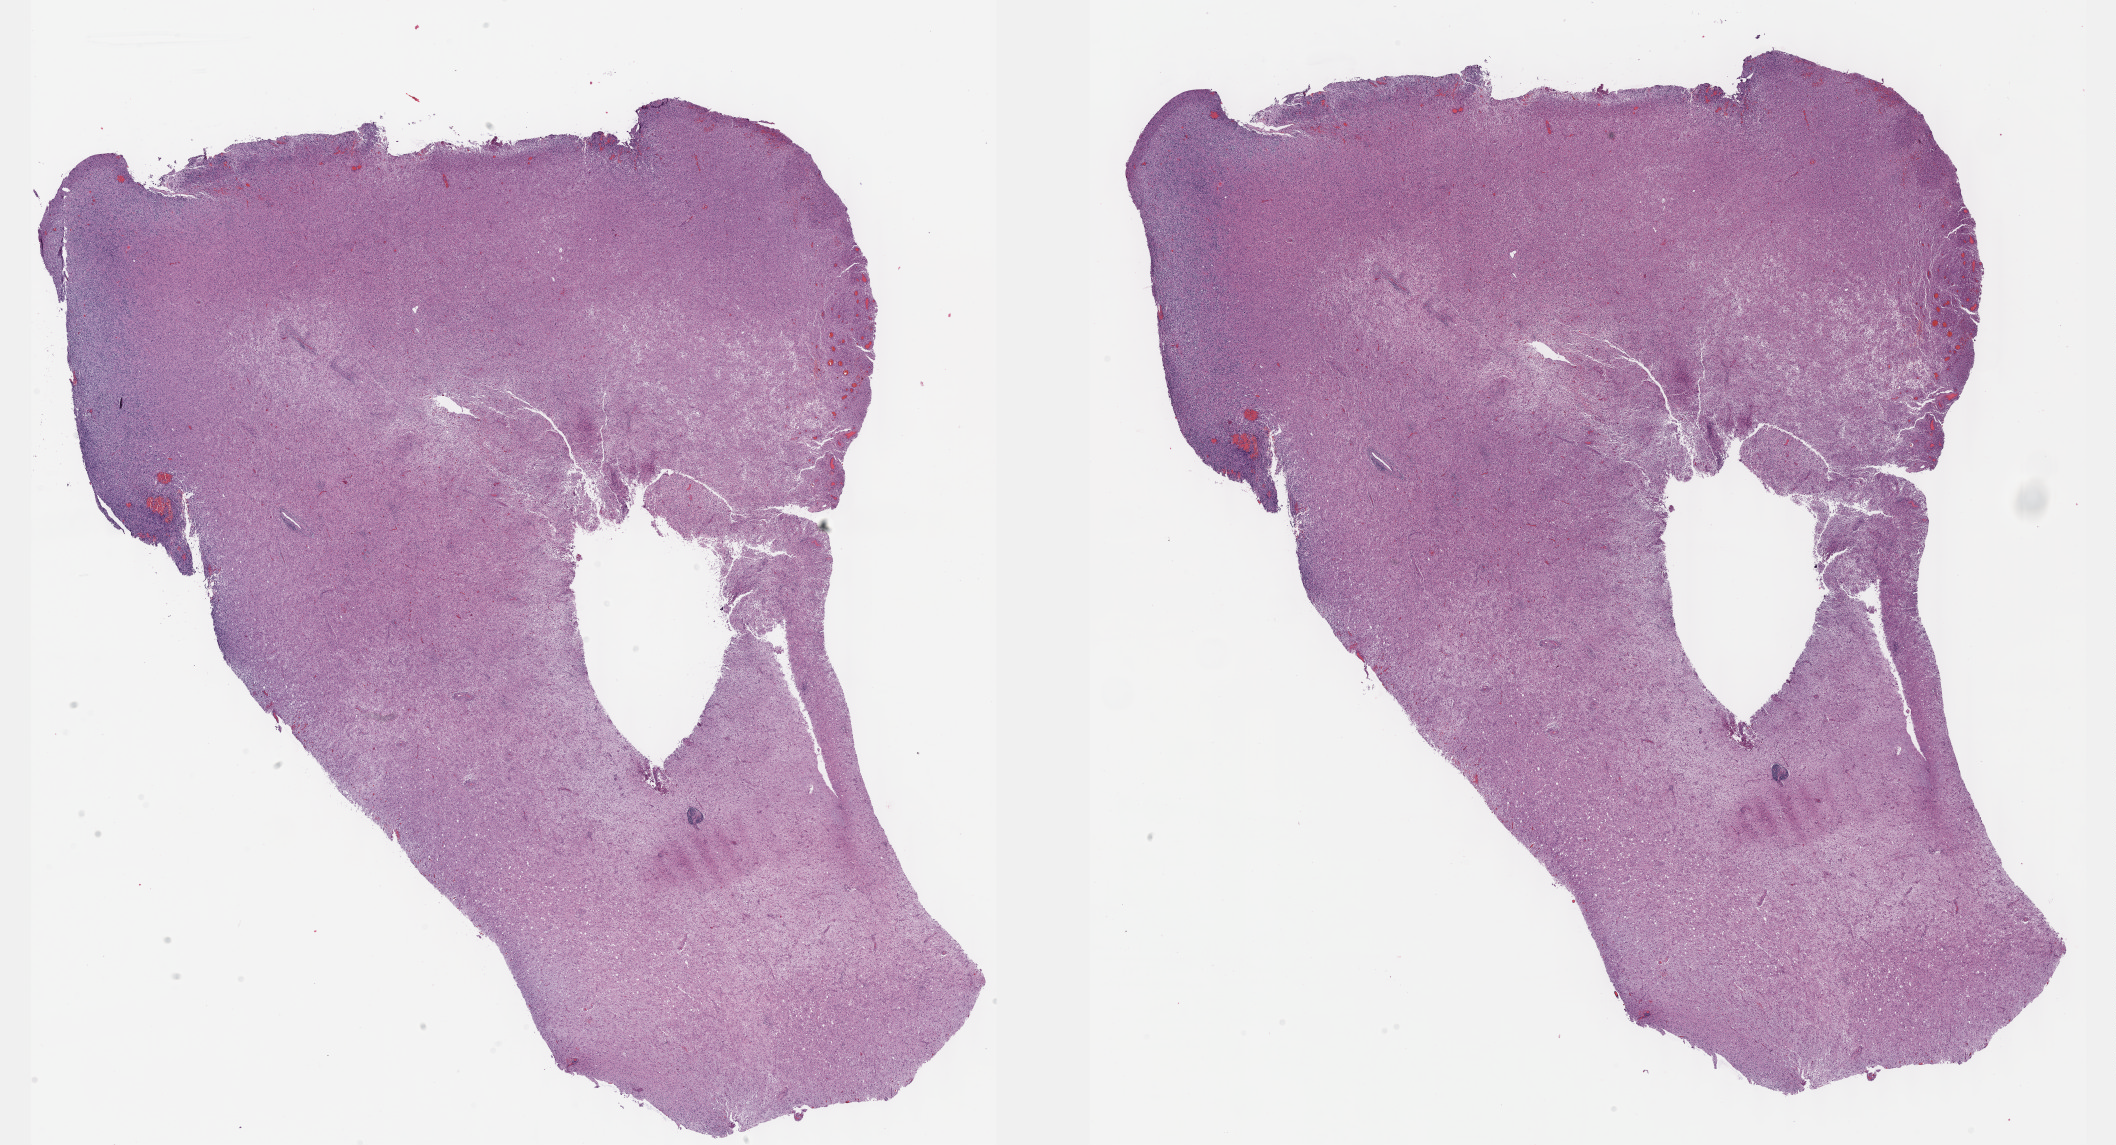
Whole-slide histology image, H&E-stained — a low-resolution overview of the entire scanned area, about 34.2 x 18.5 mm; formalin-fixed paraffin-embedded (FFPE) diagnostic section; primary tumour sample from the brain. Patient: female, age at initial diagnosis 52 years.
Histologic diagnosis: Astrocytoma, anaplastic (cerebrum).